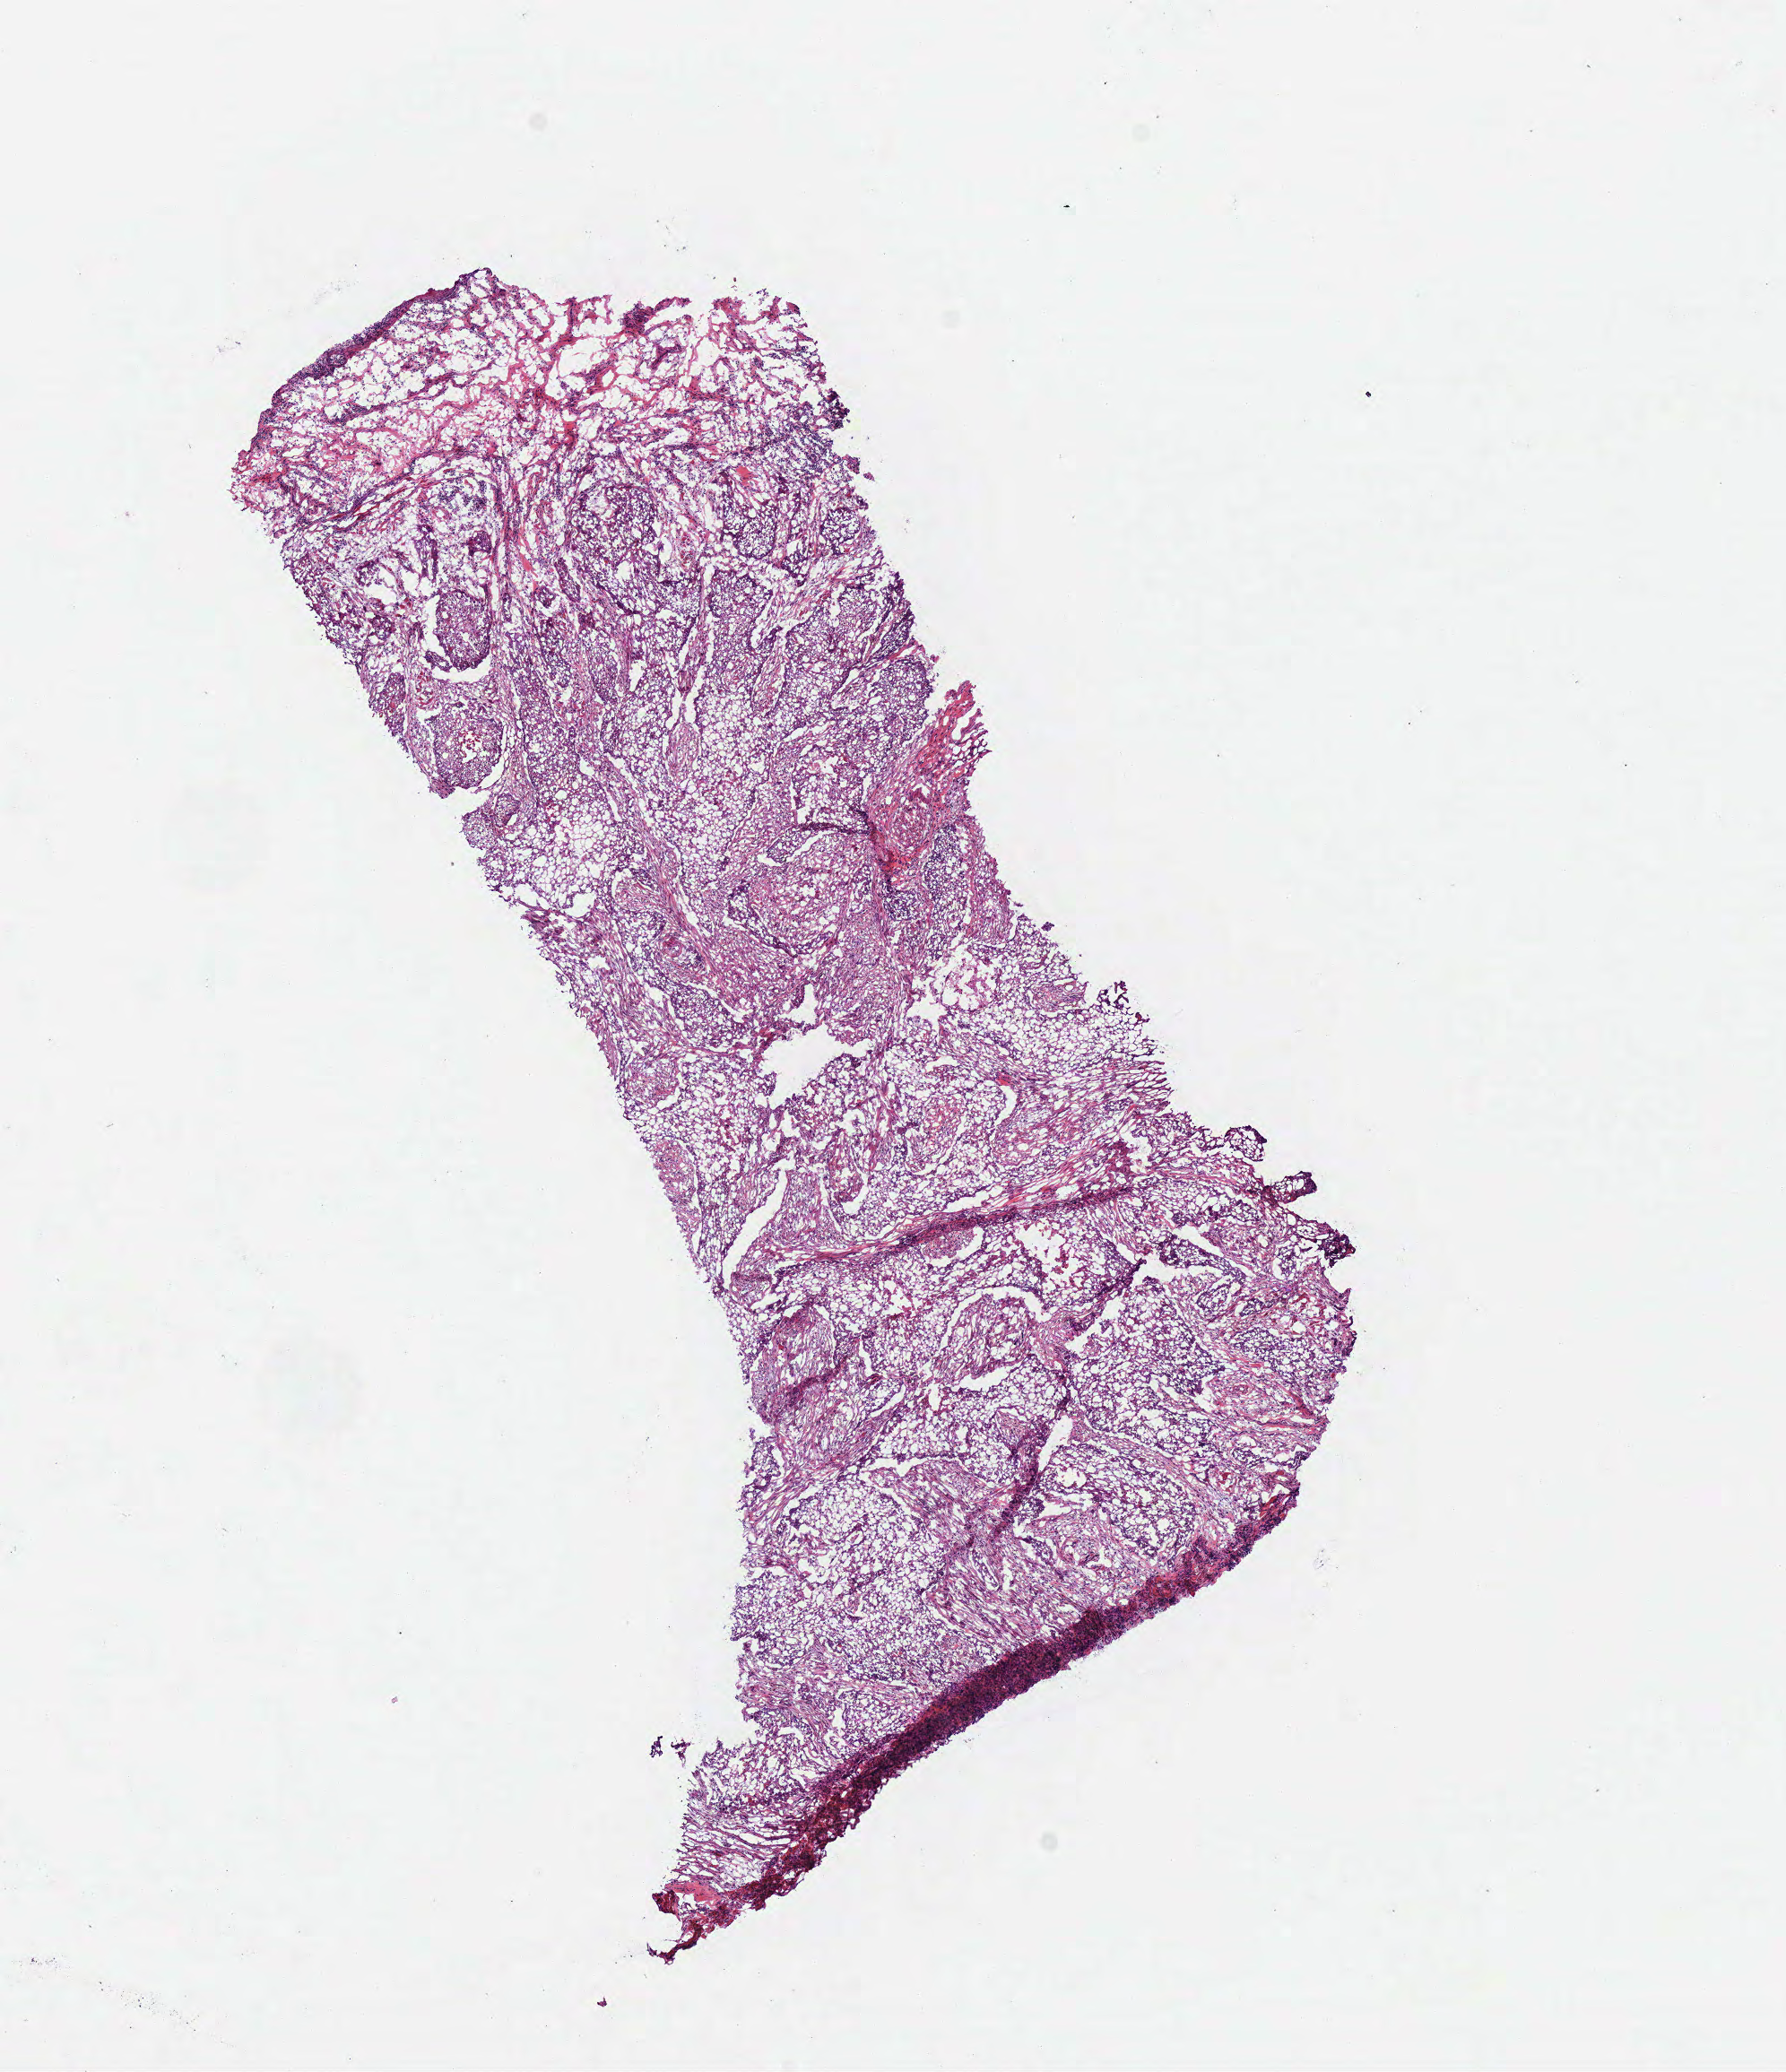
Whole-slide histology image, Hematoxylin and eosin (H&E) stained, shown as a low-resolution overview of the whole scanned area (about 7.8 x 9.1 mm, from a 40x scan). Frozen section. Sample: primary tumour, head and neck. Male patient; age at initial diagnosis 49 years. Histologic grade: G2 (moderately differentiated). Slide review estimates, as recorded: tumour cells 80%, tumour nuclei 70%, normal cells 0%, stromal cells 20%, necrosis 0%.
AJCC pathologic stage: IVA. Pathologic diagnosis: Squamous cell carcinoma, NOS (tongue, NOS). Lymph nodes positive (case pathology): 2 of 14 examined.